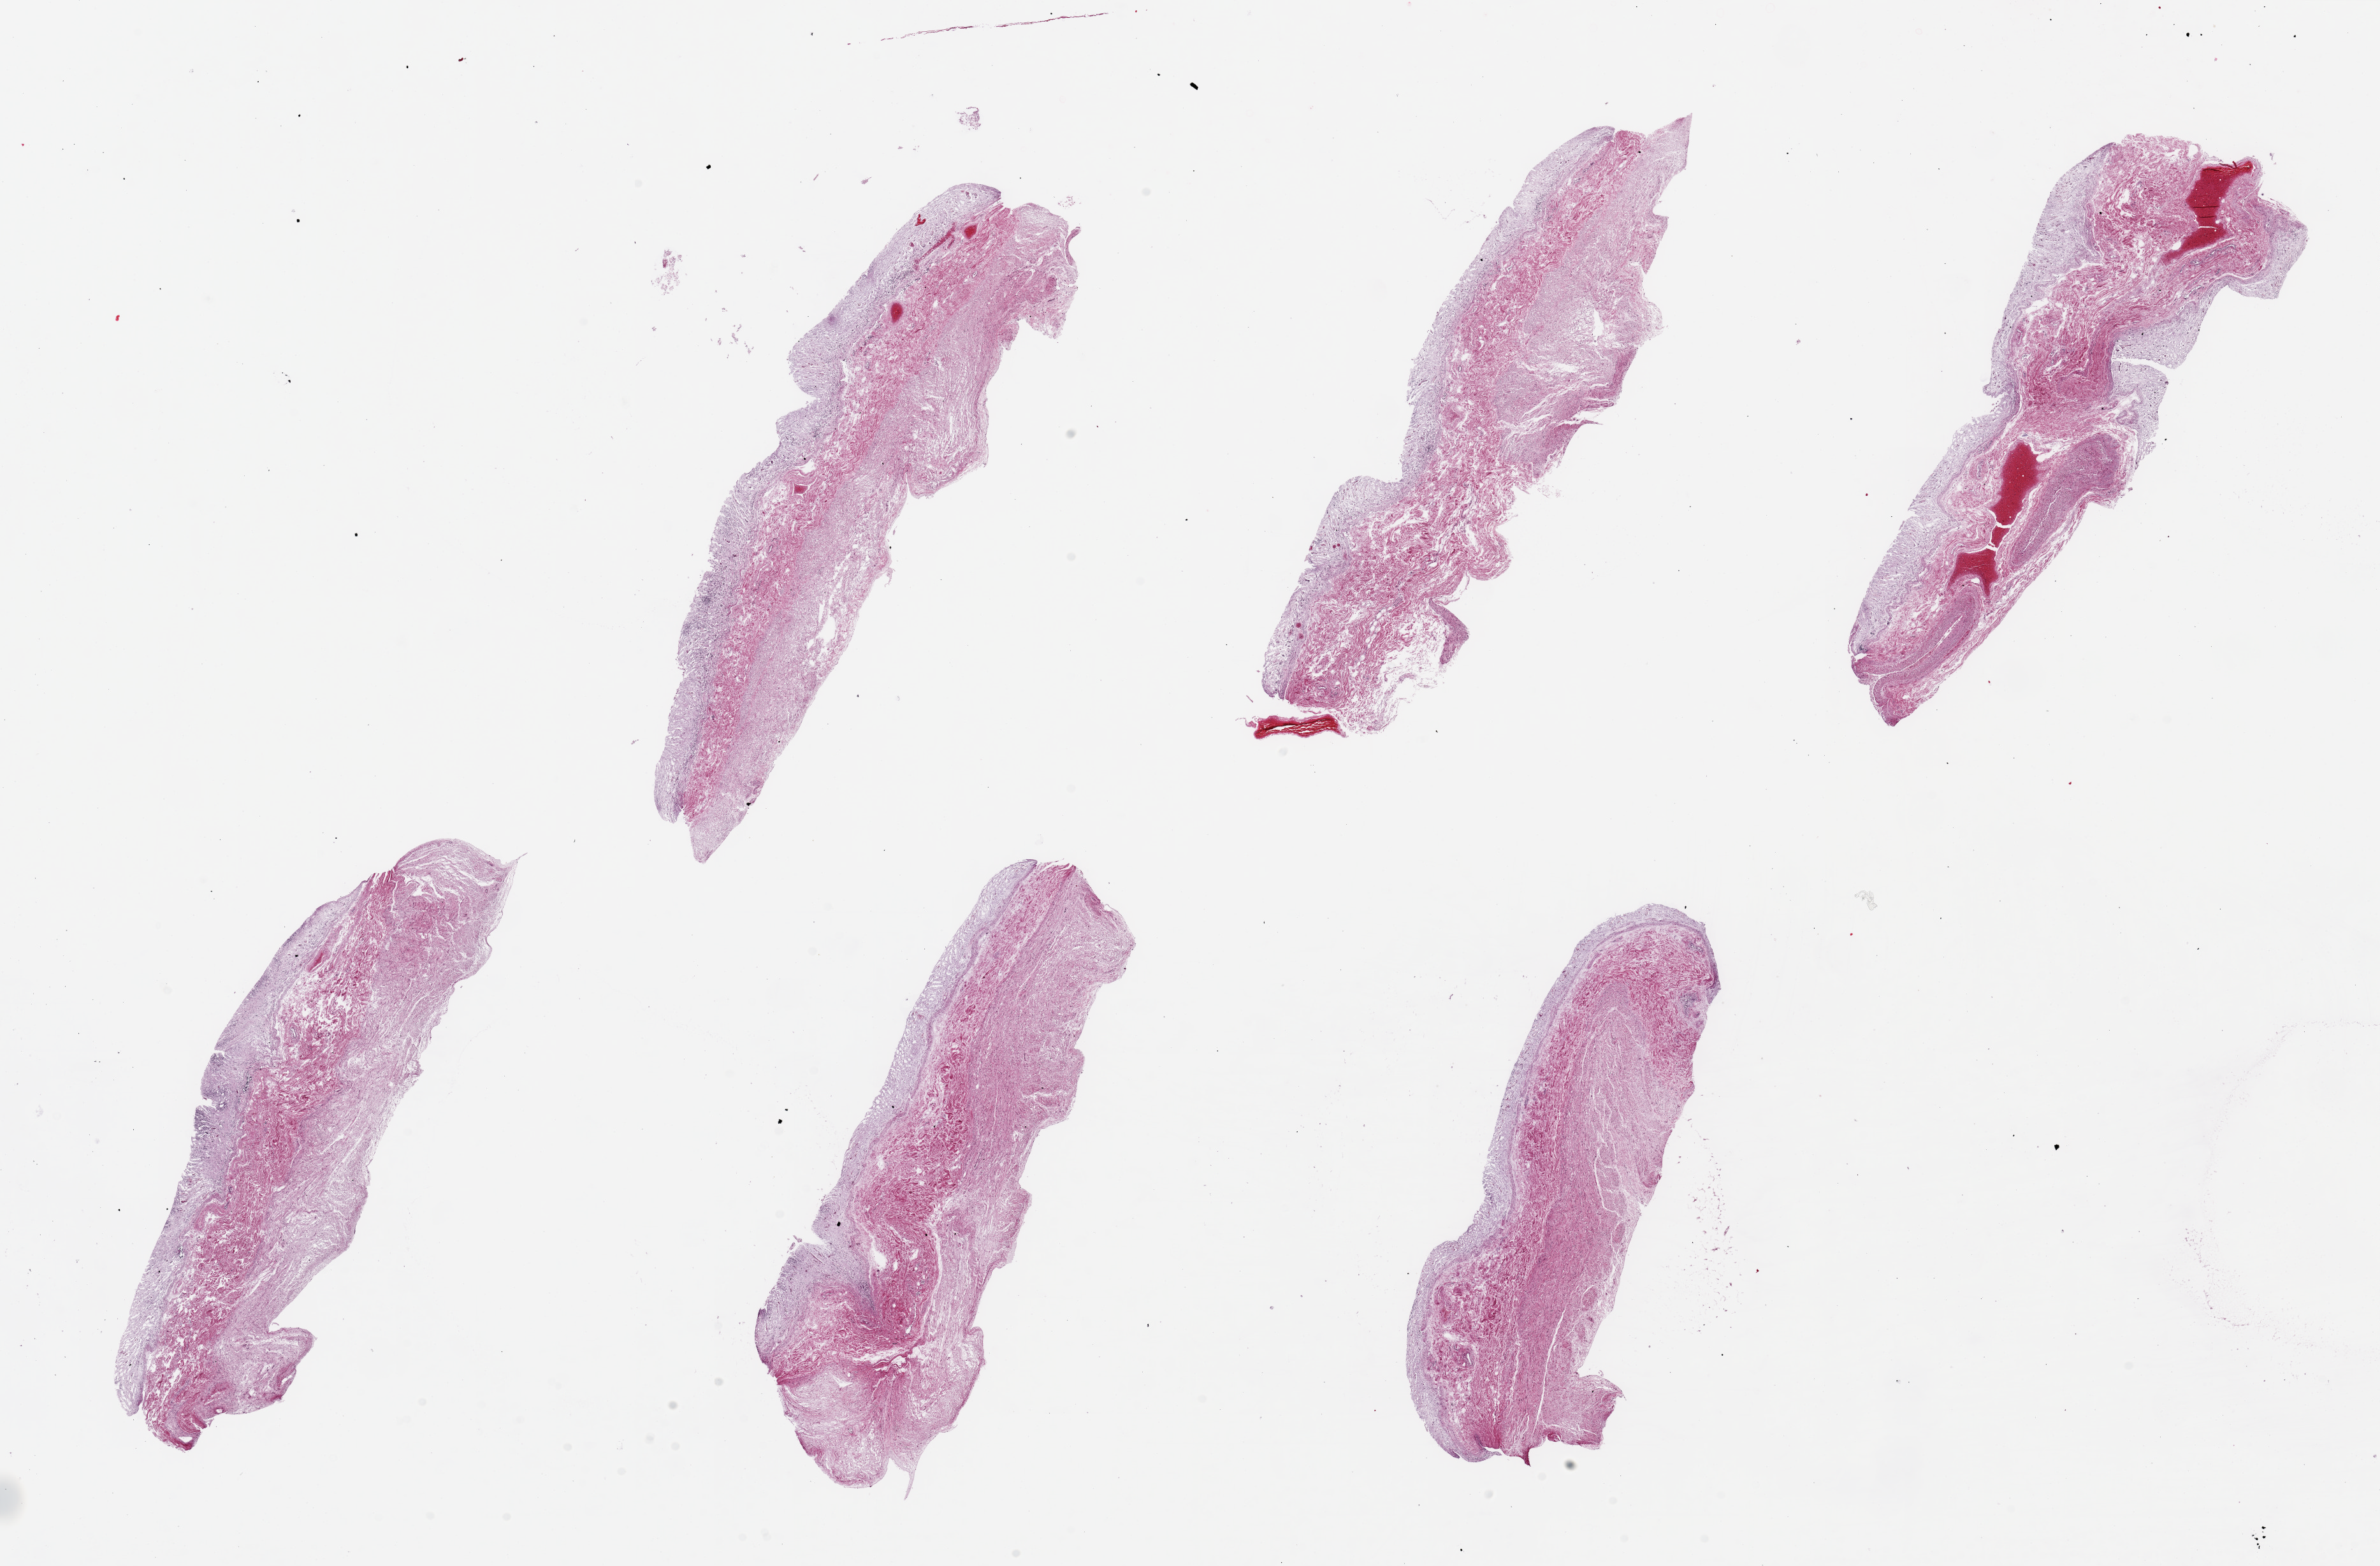
Hematoxylin and eosin (H&E) whole-slide image, brightfield, a low-resolution overview of the entire scanned area, about 29.5 x 19.4 mm, PAXgene-fixed paraffin-embedded (PFPE) section, sampled site (target tissue): stomach, tissue donor sample. Donor: male.
Pathologist's review note for this sample: 6 pieces, up to 9x2mm; too autolyzed for further study.